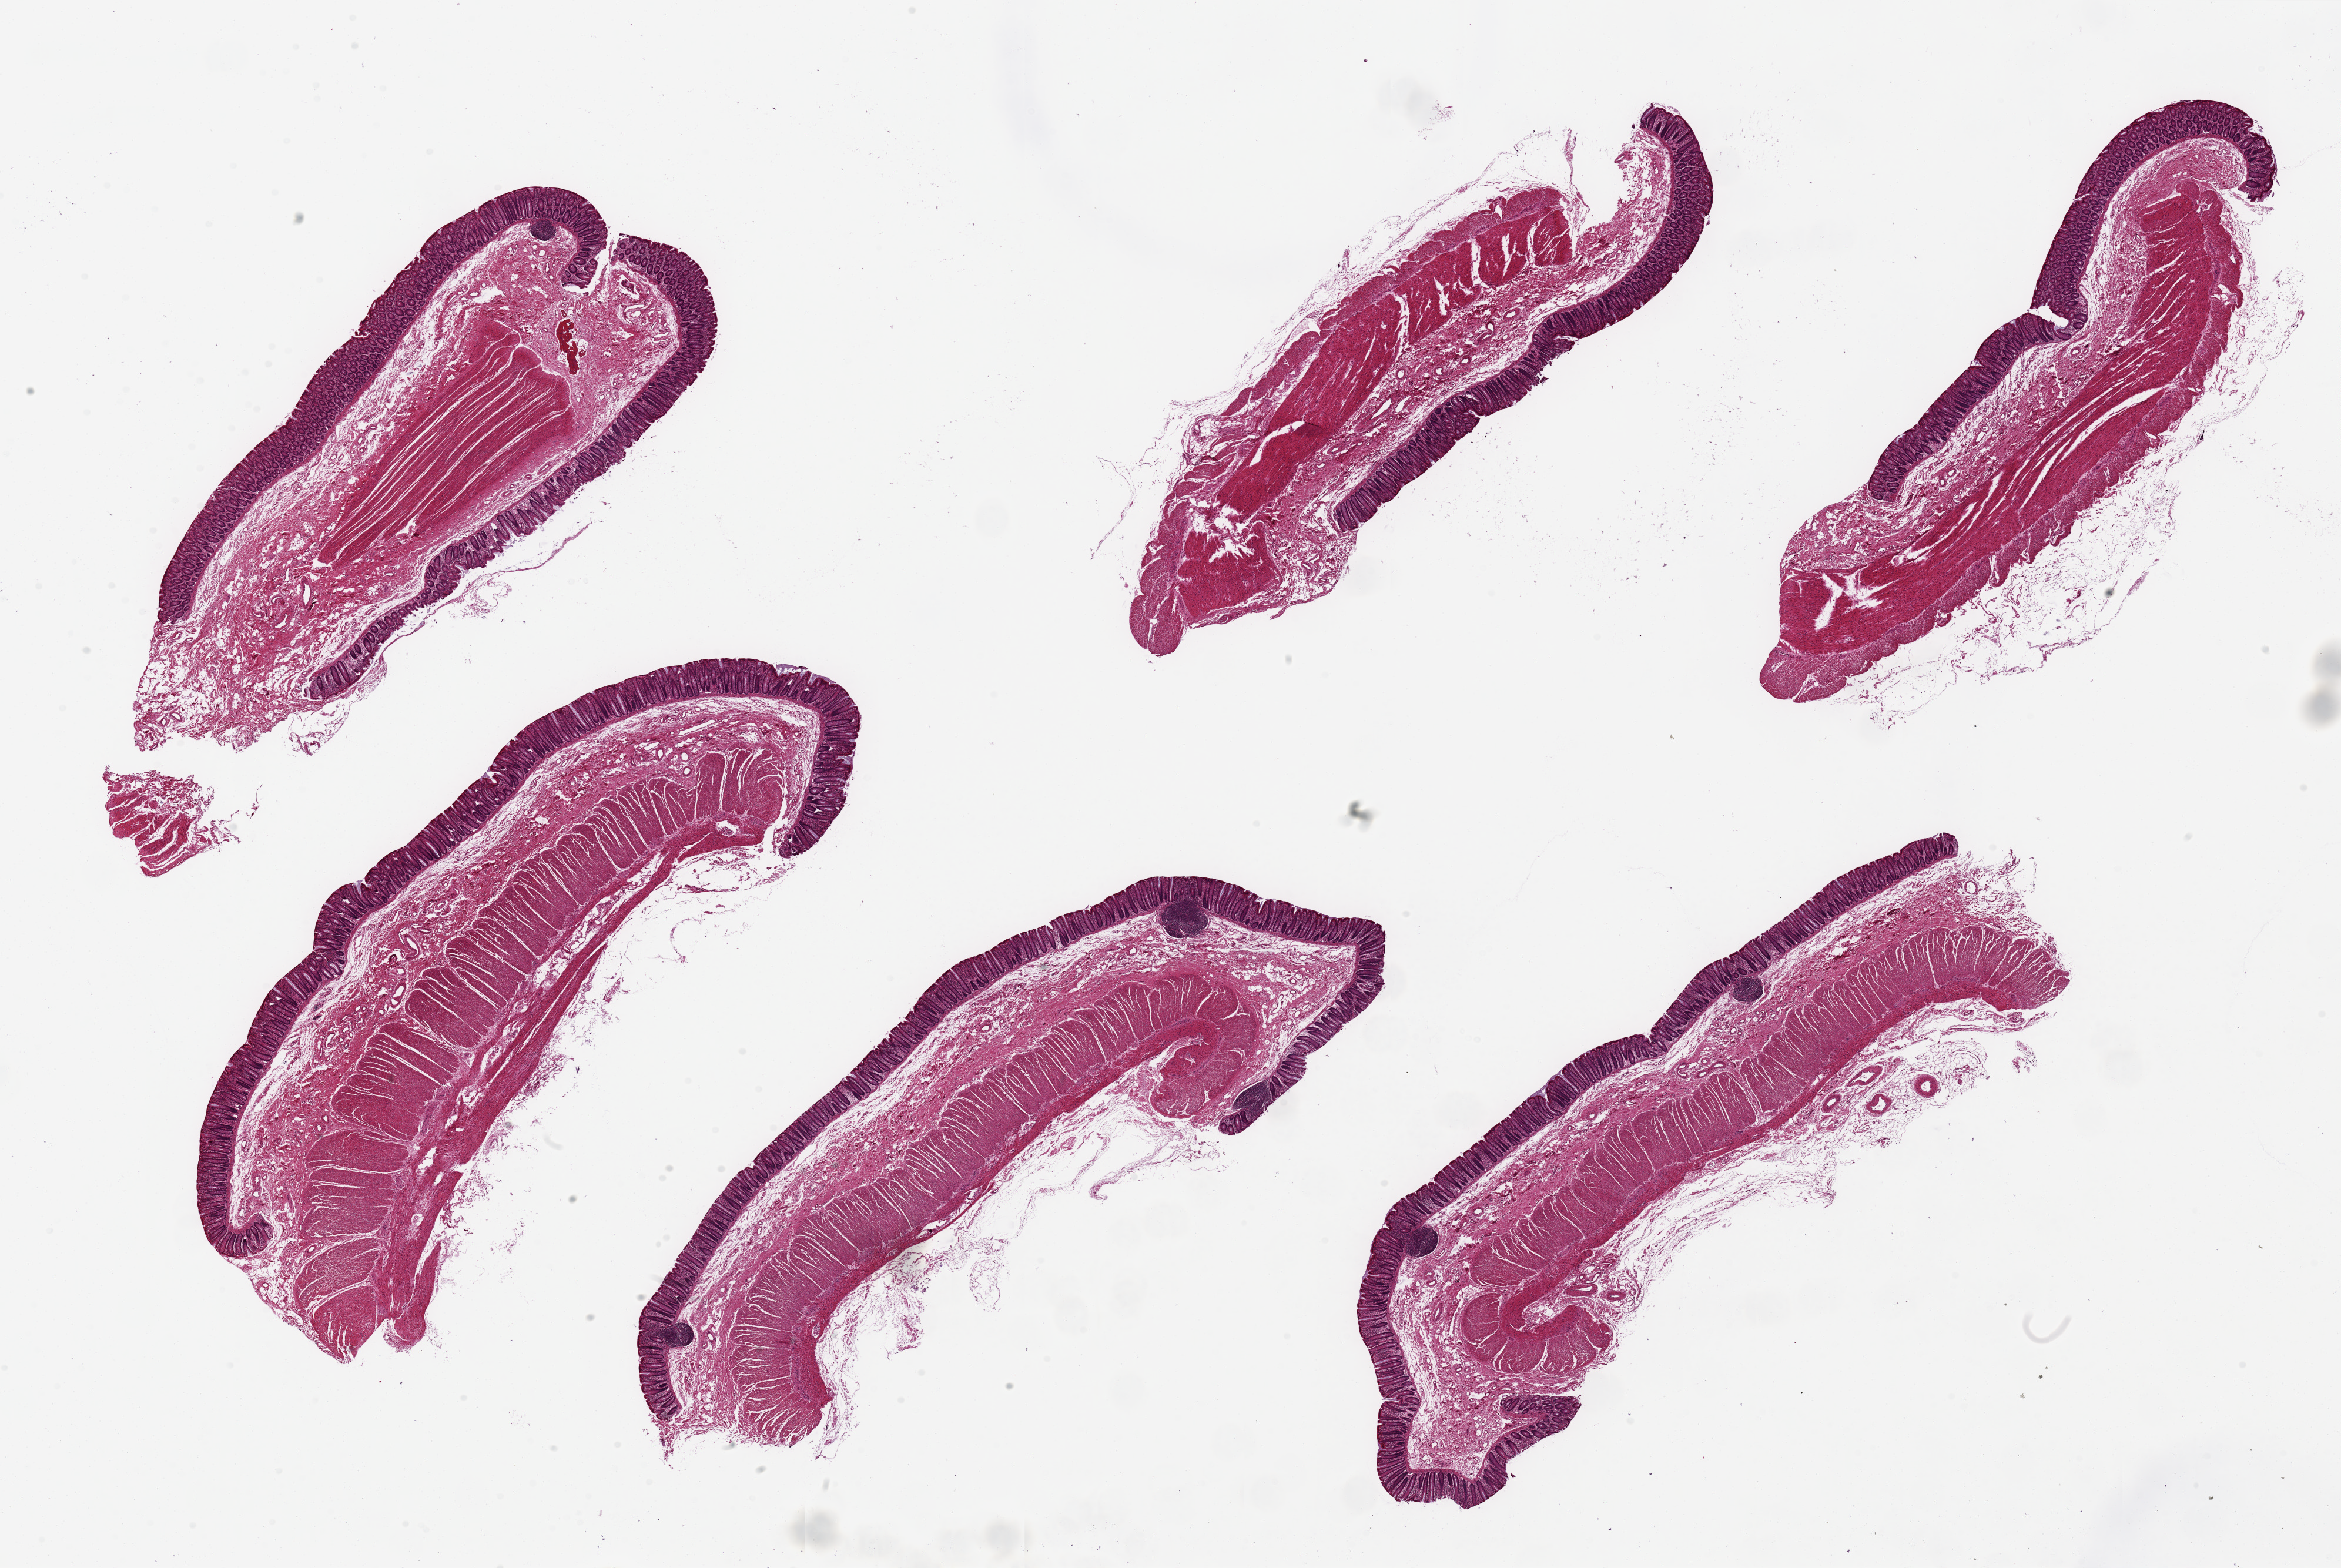
Whole-slide image, H&E stain, brightfield, shown as a low-resolution overview of the whole scanned area (about 31.5 x 21.1 mm, from a 20x scan). PAXgene-fixed paraffin-embedded (PFPE) section. Sampled site (target tissue): transverse colon. Tissue donor sample. Male donor.
Pathologist's review note for this sample: 6 pieces up to 11x4 mm; each has well preserved mucosa and all layers intact.